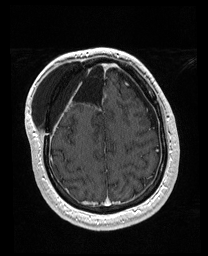
Brain MRI from a brain-tumour surgery series, one axial slice. Position 52 of 176 along the scan axis. T1-weighted post-contrast. 1 mm slice thickness. 208 × 256 image matrix, field of view 208 × 256 mm. Case-level facts recorded for this patient, not image findings: histopathology: Astrocytoma; WHO grade: 4; IDH mutation: yes.
Structures marked on this image (manually delineated by an expert):
- previous resection cavity: bounding box [x1, y1, x2, y2] px = [56, 61, 106, 103]